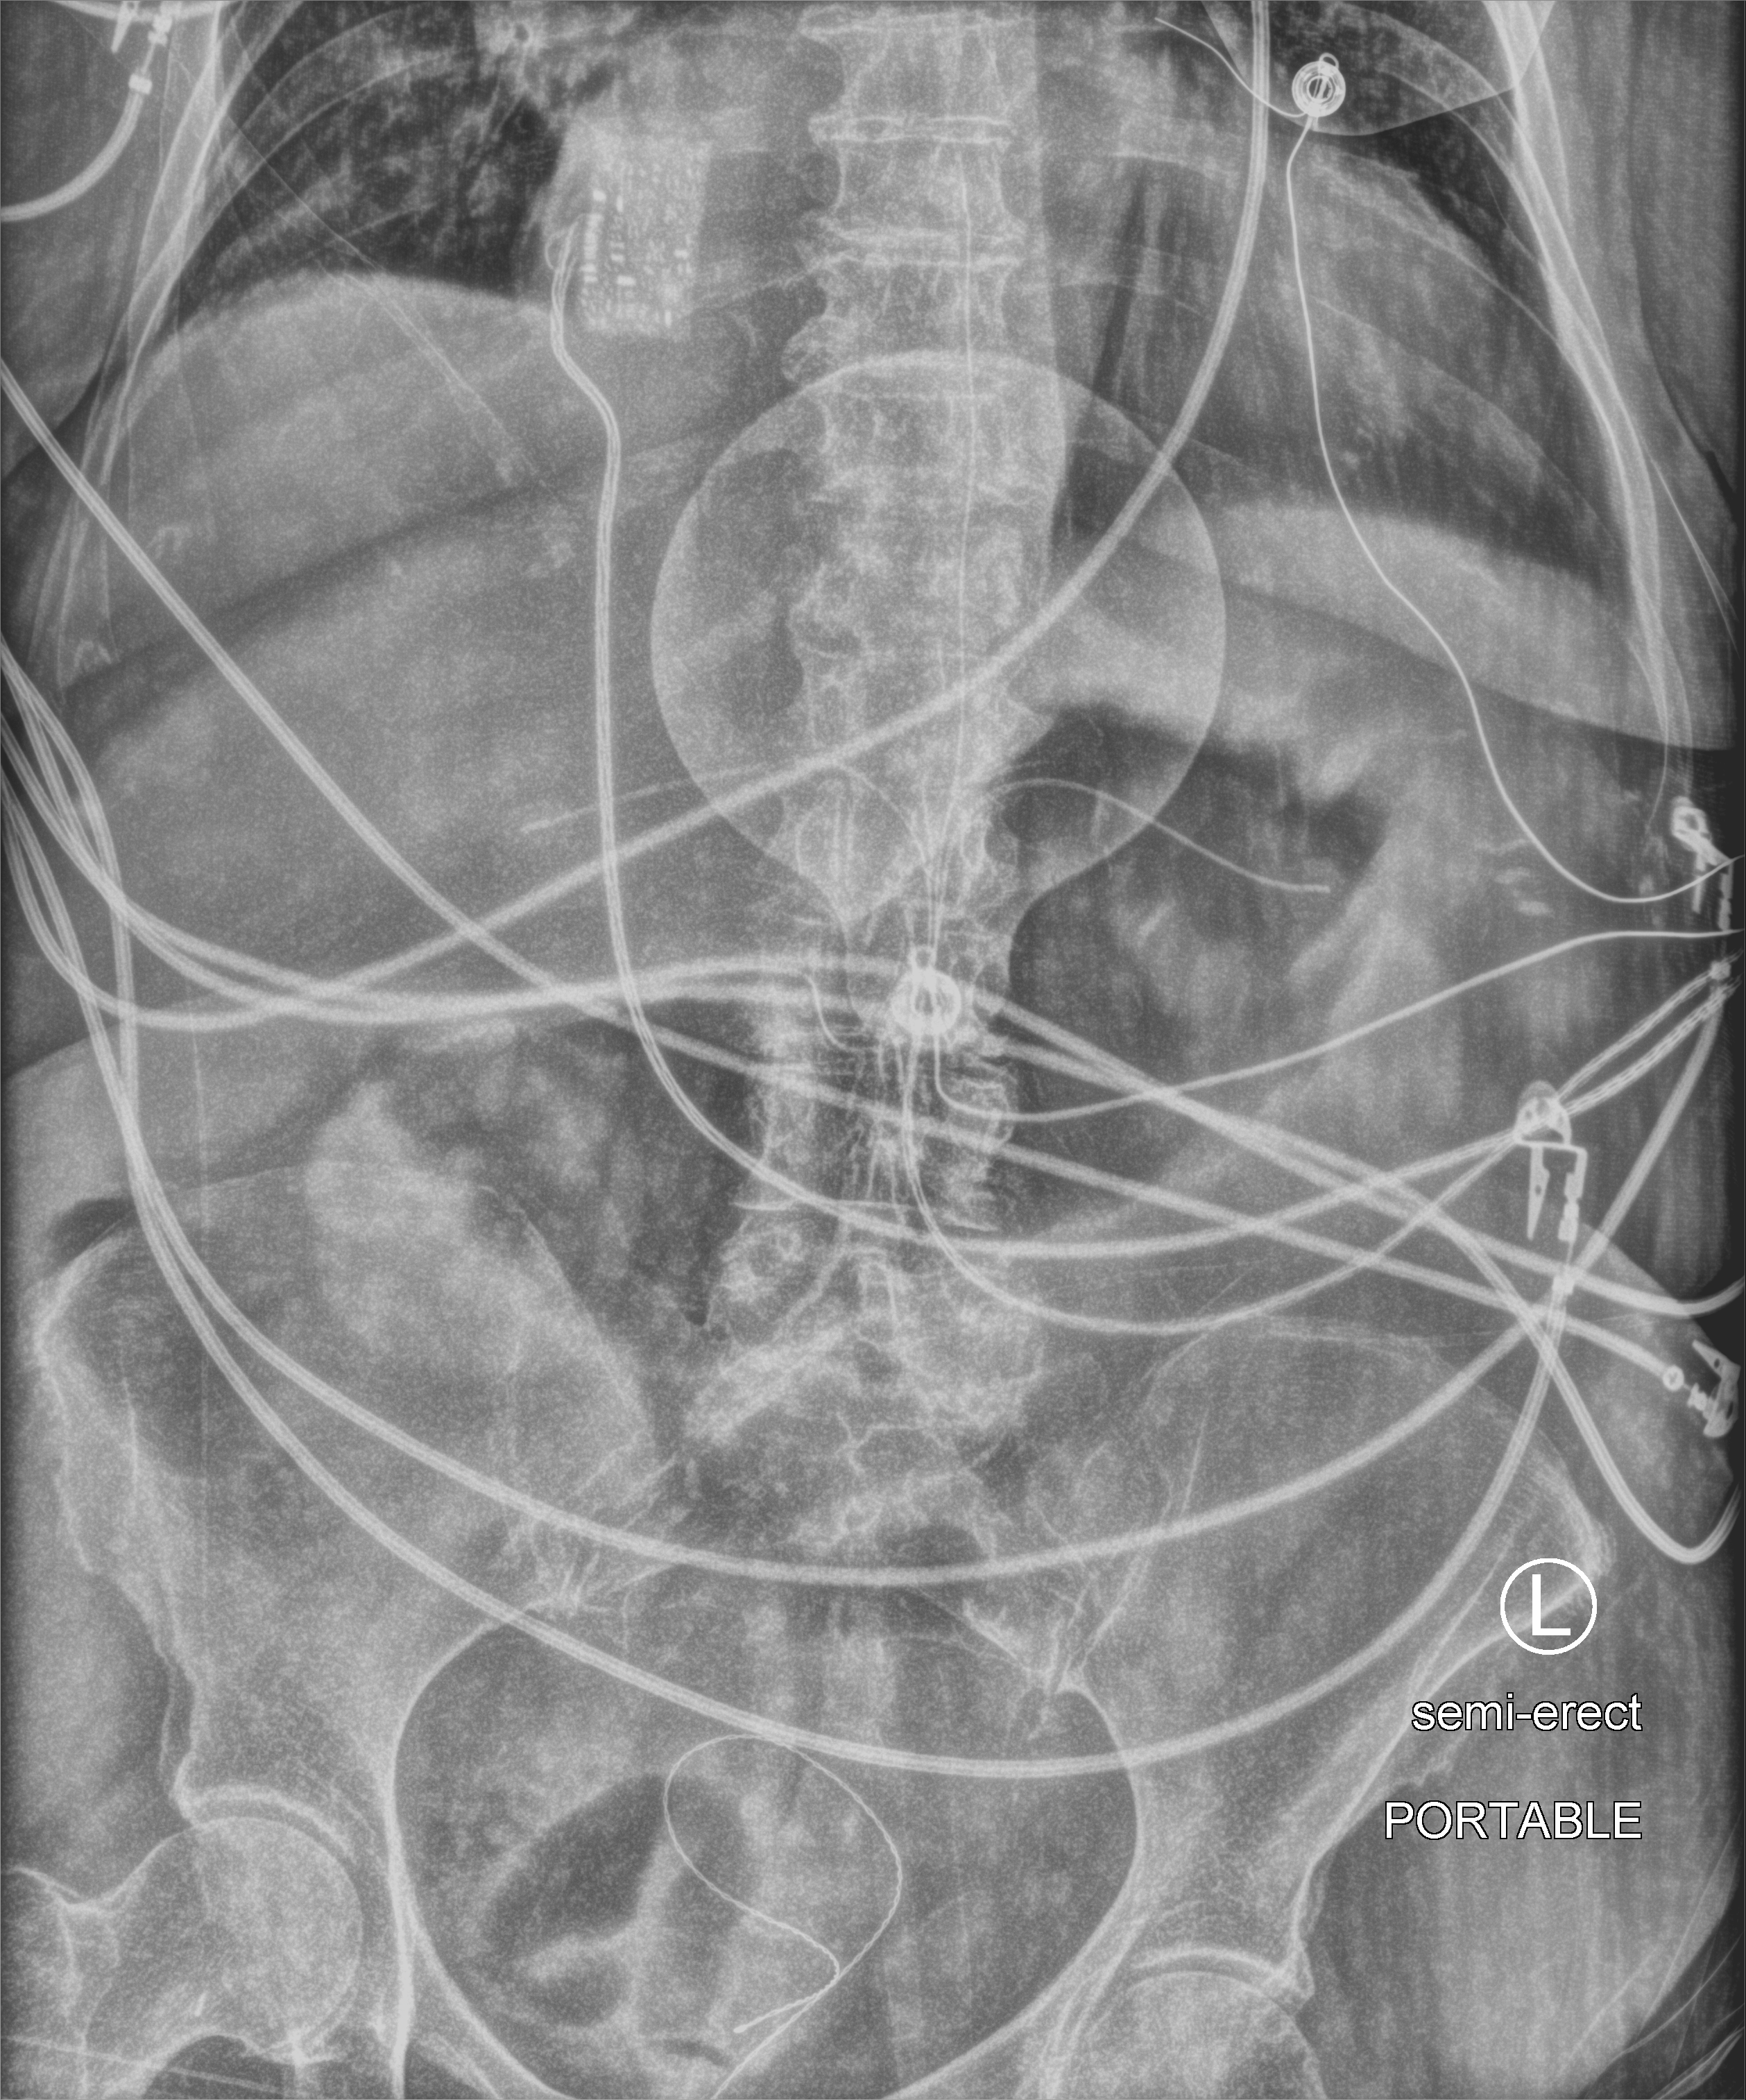
Bedside abdomen radiograph (computed radiography); anteroposterior (AP) projection. Patient hospitalised with COVID-19; female, aged 75–90 years.
Admission-level facts for this patient (not findings on this image; timing relative to this image not recorded): COPD (admission record): yes; mechanically ventilated during this hospital stay: no.